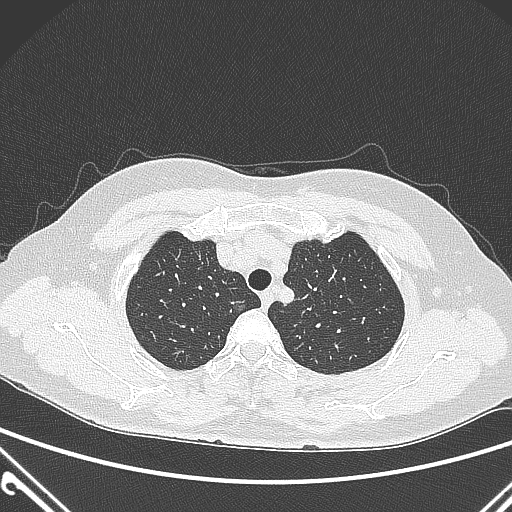
Chest CT, one axial slice; position 234 of 300 along the scan axis; 120 kVp; lung window (W 1500 / L -600 HU); 512 × 512 image matrix, field of view 350 × 350 mm. Patient: female, 54 years. Case-level facts recorded for this patient, not image findings: clinical TNM (as recorded): T1a N0 M0.
Outlined on this slice (rectangle marked by the reading radiologist):
- lung tumour (recorded histology: adenocarcinoma): bounding box <229,294,256,322> (left, top, right, bottom; pixels)